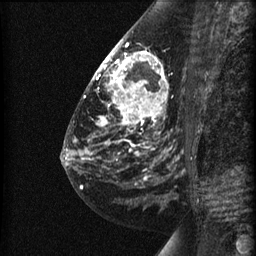
Breast MRI (dynamic contrast-enhanced), one sagittal slice. Slice 29 of 60 in the series (ordered by position). Dynamic contrast-enhanced series, image 2 of 3 at this slice position (ordered by acquisition). 1.5 T. TE 4.2 ms, TR 22.7 ms. 256 × 256 image matrix, field of view 180 × 180 mm. Patient: female, 48 years. From the clinical record (not read from this slice): setting: breast cancer imaged before/during neoadjuvant chemotherapy; receptor status: triple-negative.
Structures marked on this image (semi-automatic segmentation, software-assisted and operator-edited):
- analysis volume of interest (the breast-tissue region the enhancement analysis was run in; not a lesion): bounding box [x1, y1, x2, y2] px = [89, 27, 191, 180]
- tumour enhancement mask (voxels above the 90 % enhancement threshold inside the analysis volume of interest): [94, 40, 166, 154]